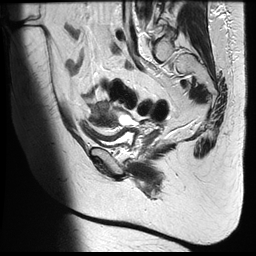
Pelvic MRI for cervical cancer, one sagittal slice. Position 22 of 35 along the scan axis. T2-weighted. 1.5 T. TE 122.8 ms, TR 4992 ms. 4 mm slice thickness. 256 × 256 image matrix. Patient: female, 42 years.
Annotated regions visible in this slice (outlined manually by an expert reader):
- uterus and cervix: box from (x=92, y=101) to (x=116, y=128) px